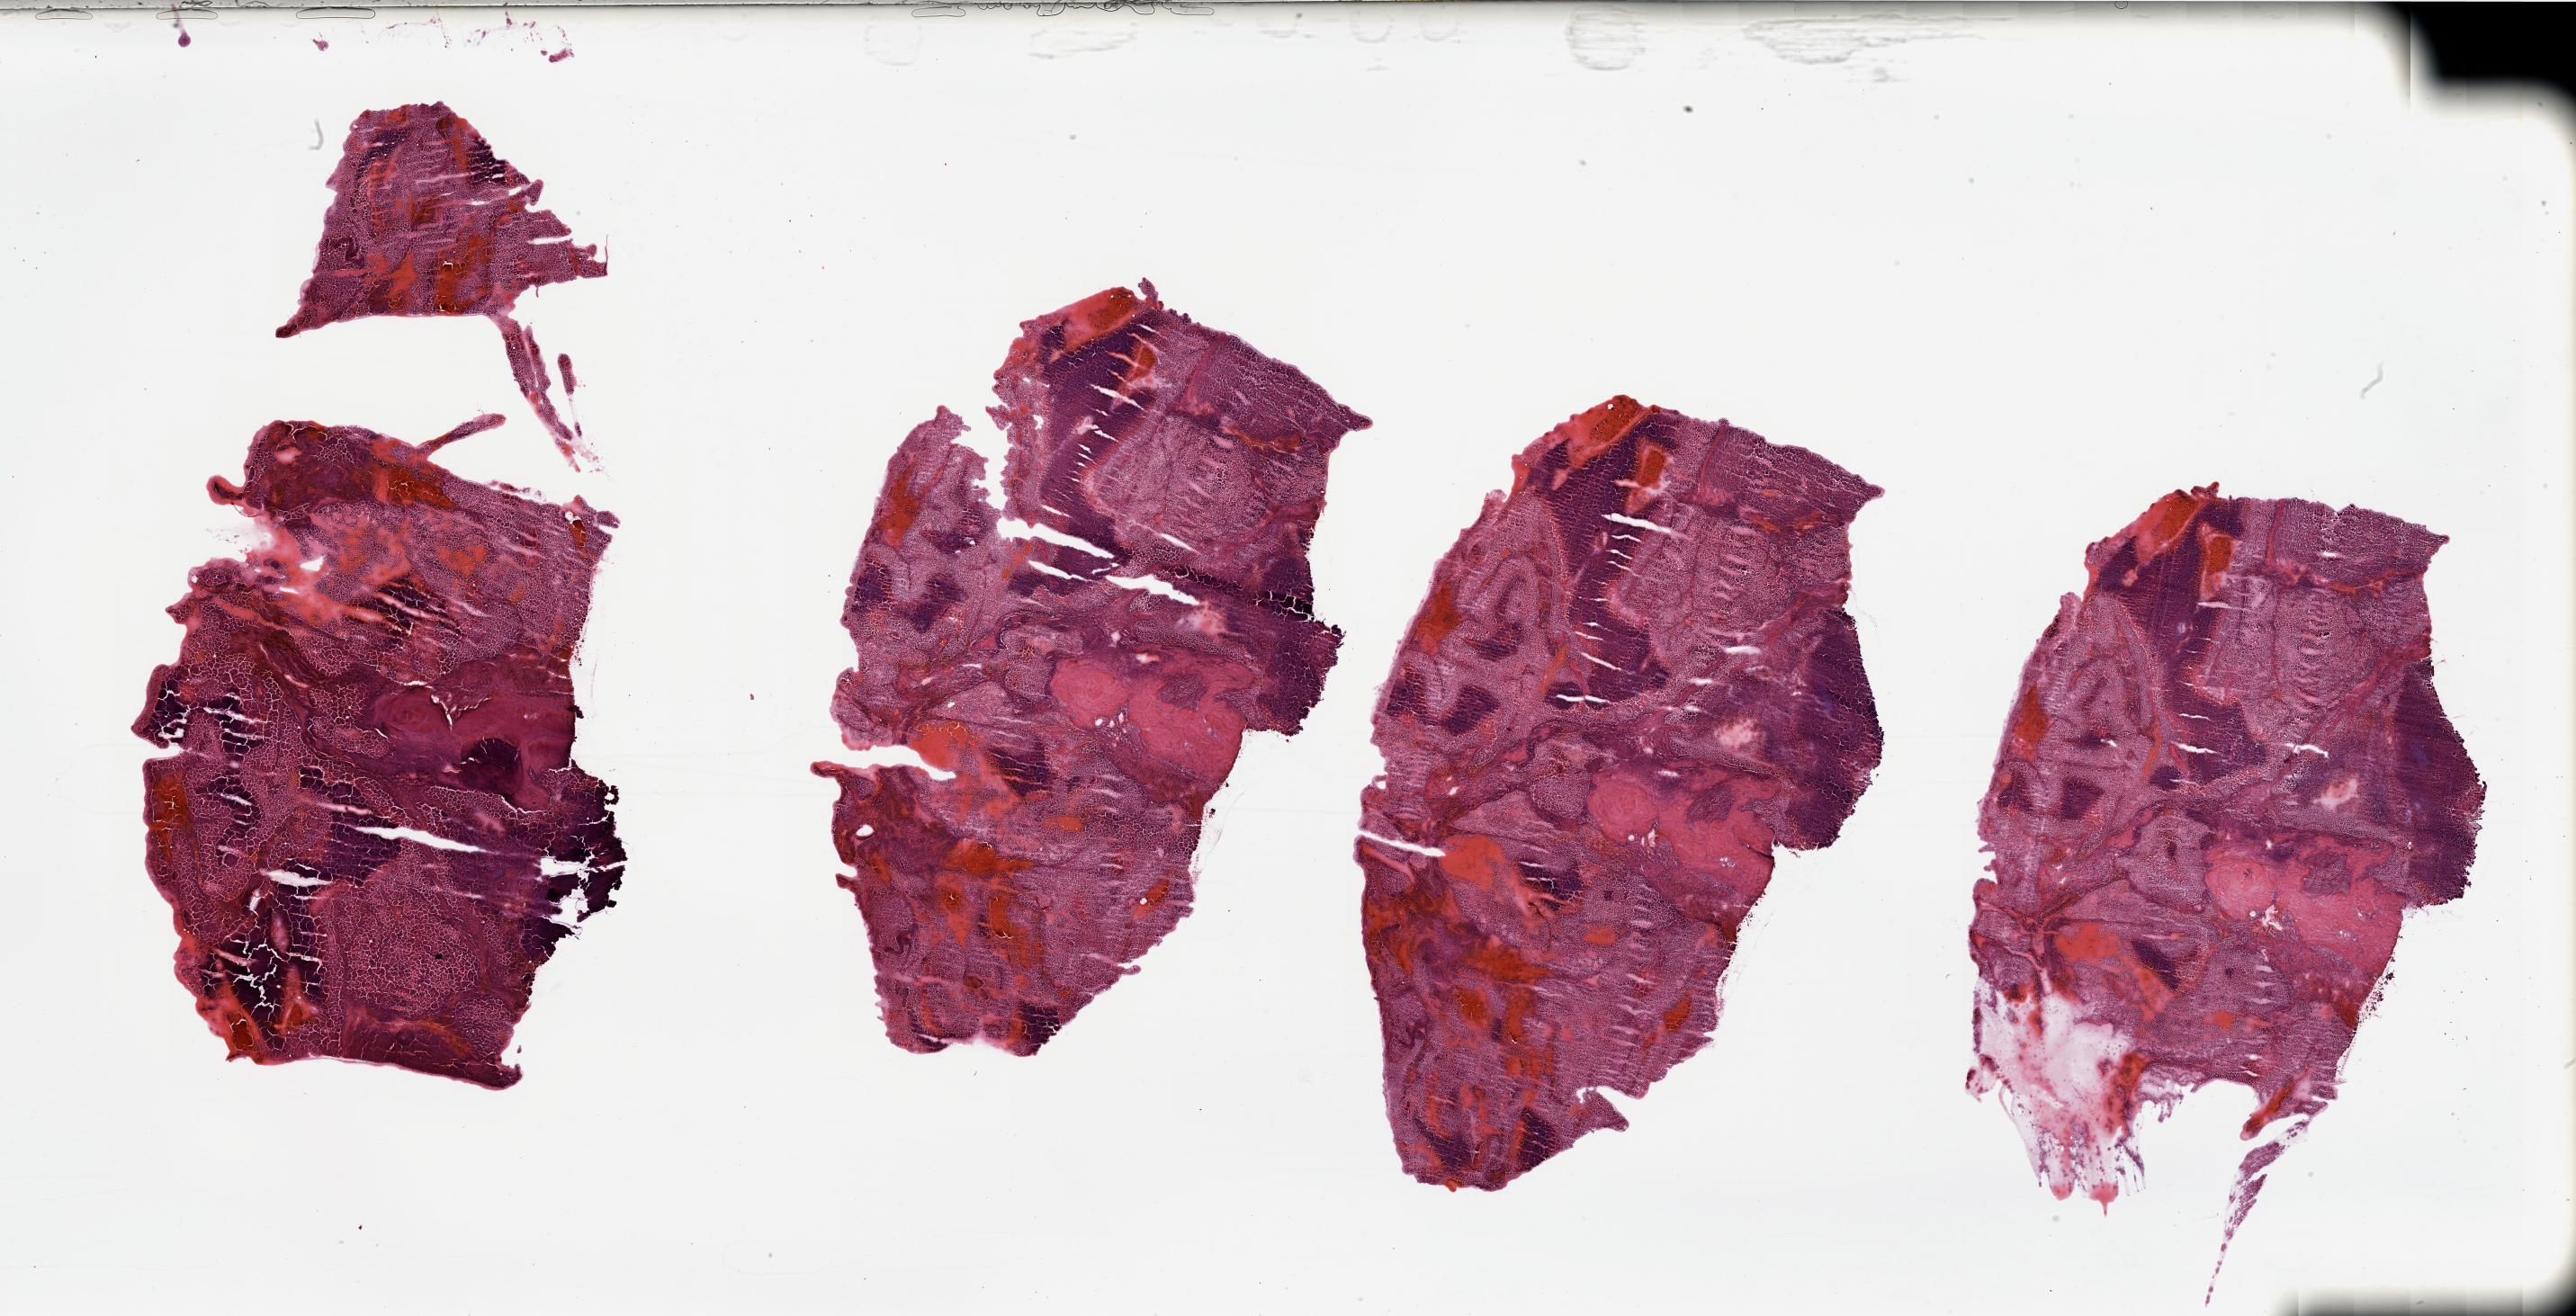
Hematoxylin and eosin (H&E) stained whole-slide image — a low-resolution overview of the entire scanned area, about 45.3 x 23.1 mm; tumour tissue sample, sampled site: kidney. 84-year-old male patient. Histologic grade: G2 (moderately differentiated). Pathologist review of this section (percent, as recorded): tumour nuclei 75%, necrosis 30%.
* primary tumour site (as recorded): upper pole
* AJCC pathologic stage: III
* diagnosis: Renal cell carcinoma, NOS